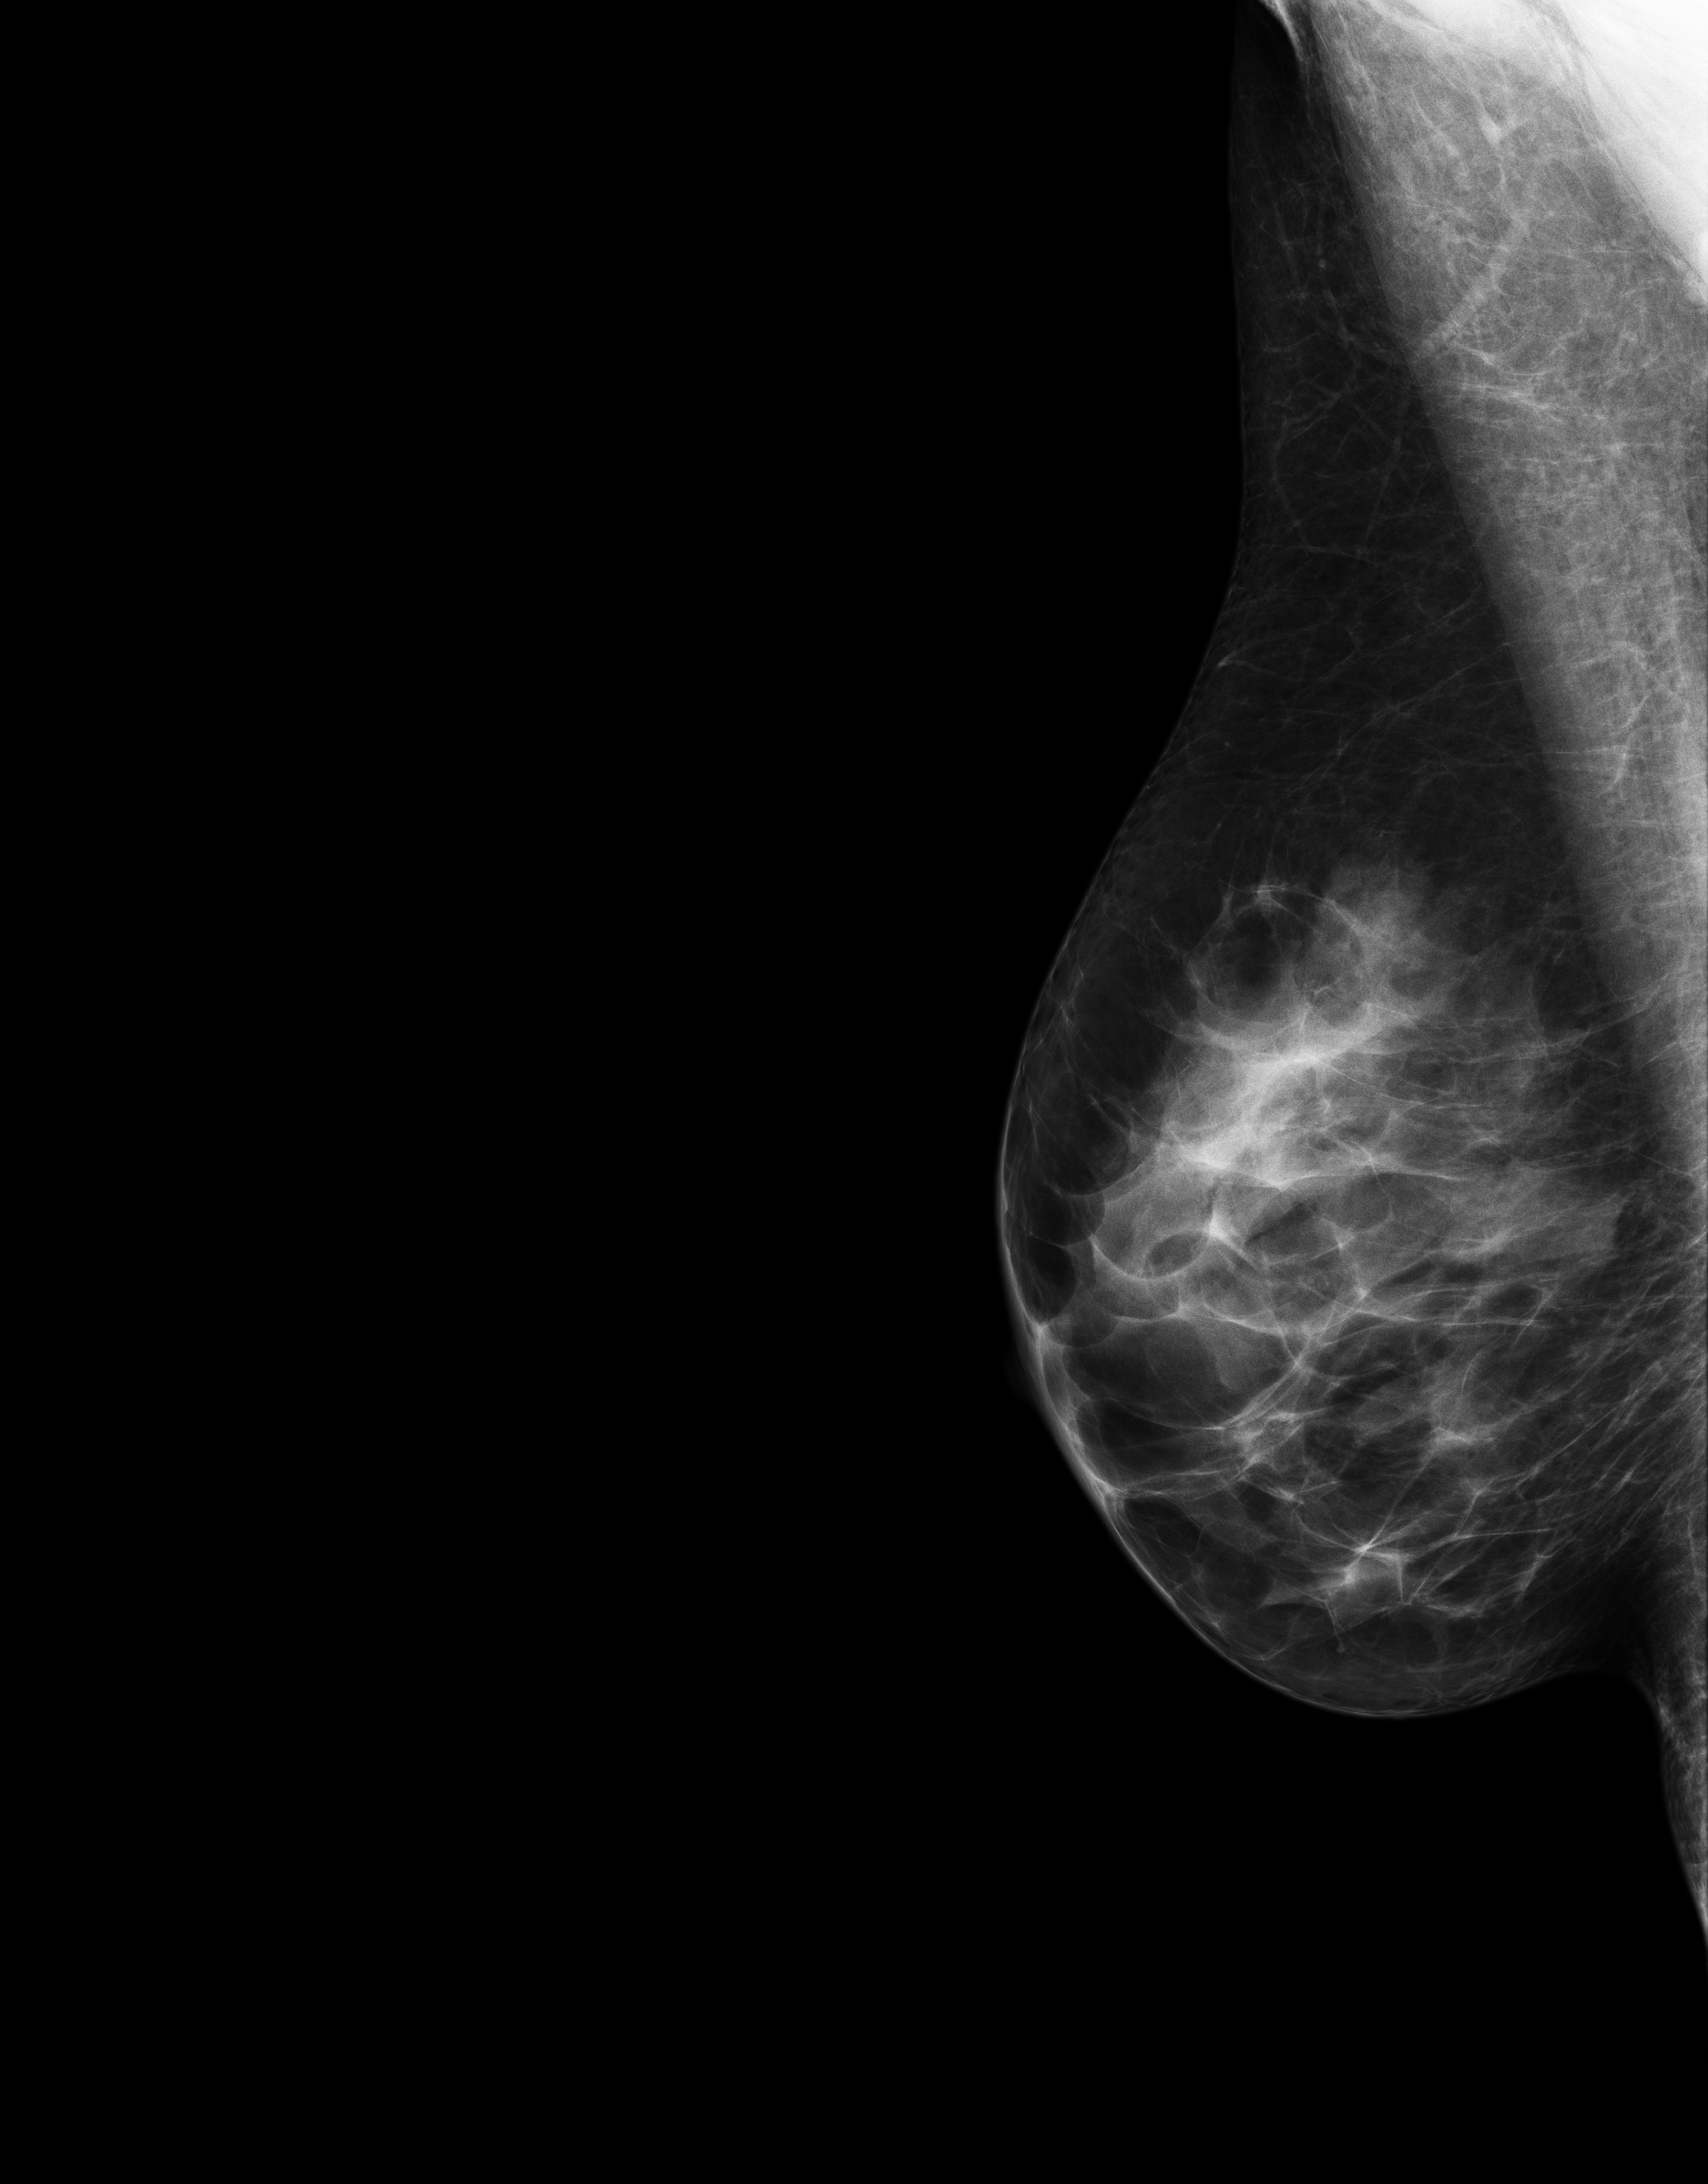
Screening examination. Patient aged 52 years (female).
Image type: full-field digital mammogram. Breast: right. Projection: mediolateral oblique (MLO) view.